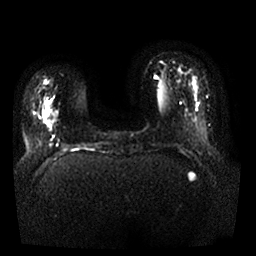
Breast MRI, one axial slice. Position 4 of 25 along the scan axis. Diffusion-weighted series; image 2 of 4 stored at this slice position (different b-values; order by instance number). 1.5 T. 4 mm slice thickness. 256 × 256 image matrix, field of view 350 × 350 mm. Female patient.
Annotated regions visible in this slice (manually delineated by an expert):
- tumour on diffusion-weighted imaging: box from (x=43, y=109) to (x=57, y=123) px